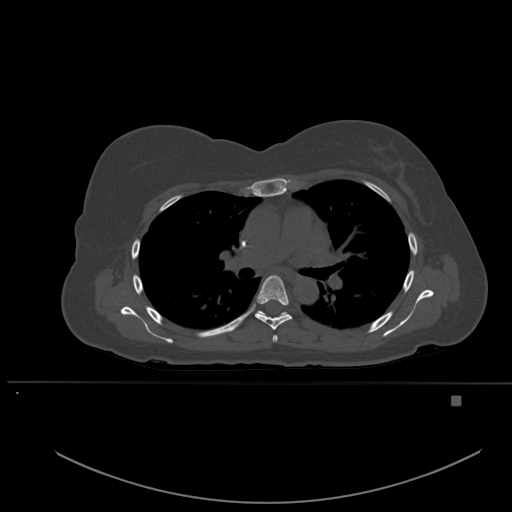
CT including the spine, one axial slice; position 363 of 651 along the scan axis; bone window (W 1800 / L 400 HU); 1.5 mm slice thickness; 512 × 512 image matrix, field of view 443 × 443 mm. Female patient, age 49 years. From the clinical record (not read from this slice): primary cancer: breast.
Annotated regions visible in this slice (semi-automatically segmented with operator editing):
- T4 vertebra: bounding box [x1, y1, x2, y2] px = [272, 335, 278, 342]
- T5 vertebra: [255, 275, 292, 330]
- T6 vertebra: [257, 311, 287, 317]